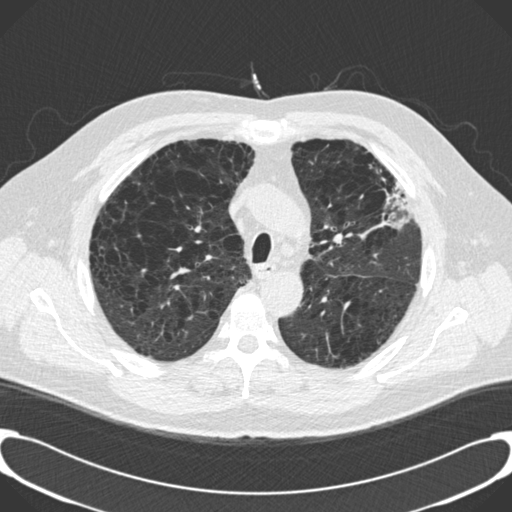
Chest CT (low-dose screening protocol), one axial image, third annual screen, lung window (W 1500 / L -600 HU), 2 mm slice thickness. Male participant, aged 59 years at enrolment. Current smoker at enrolment.
- Expert-annotated lung lesion, box from (x=359, y=155) to (x=417, y=223) px.
- No non-calcified nodule or mass ≥4 mm was recorded by the screening reader at this exam.
- Lung cancer was diagnosed 134 days after this screen: bronchiolo-alveolar carcinoma, mixed mucinous and non-mucinous, left upper lobe, stage IA (AJCC 6th edition), 20 mm at pathology.